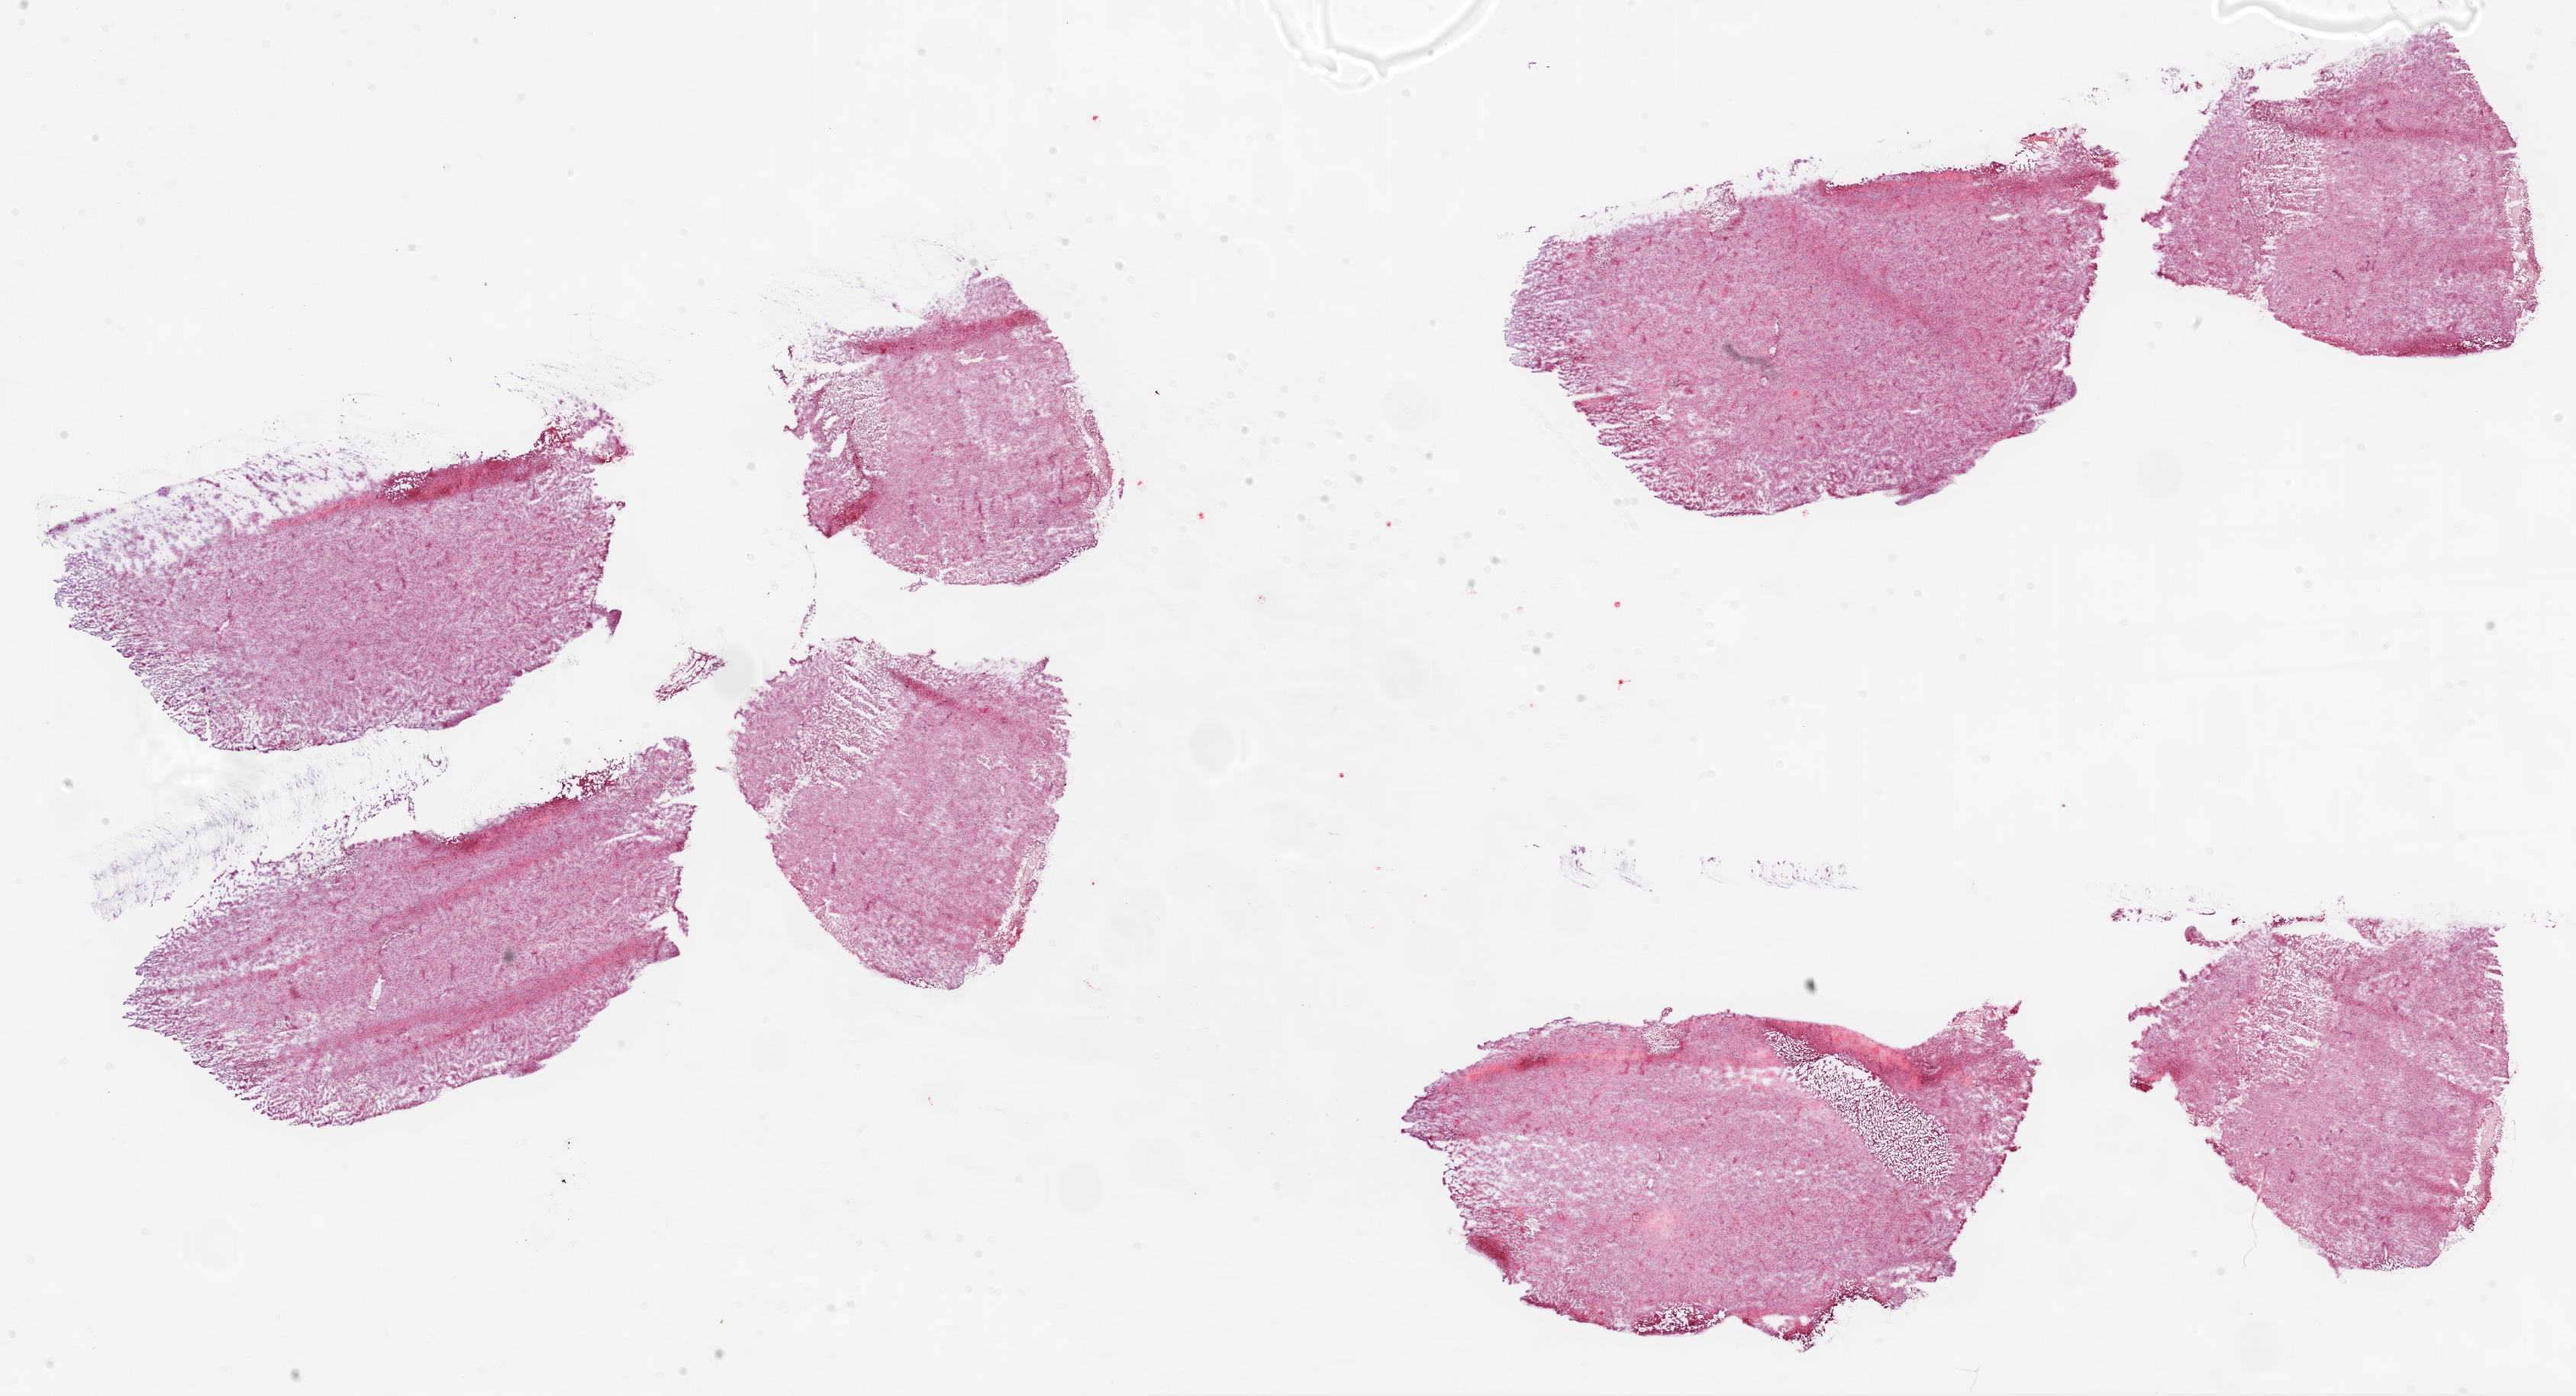
Whole-slide histology image, H&E, a low-resolution overview of the entire scanned area, about 27.1 x 14.7 mm, frozen section from the top of the tissue portion, primary tumour sample from the brain. Male patient; age at initial diagnosis 63 years. Composition of this section per pathologist review: tumour cells 95%, tumour nuclei 85%, normal cells 0%, stromal cells 0%, necrosis 5%.
Histologic diagnosis: Glioblastoma.